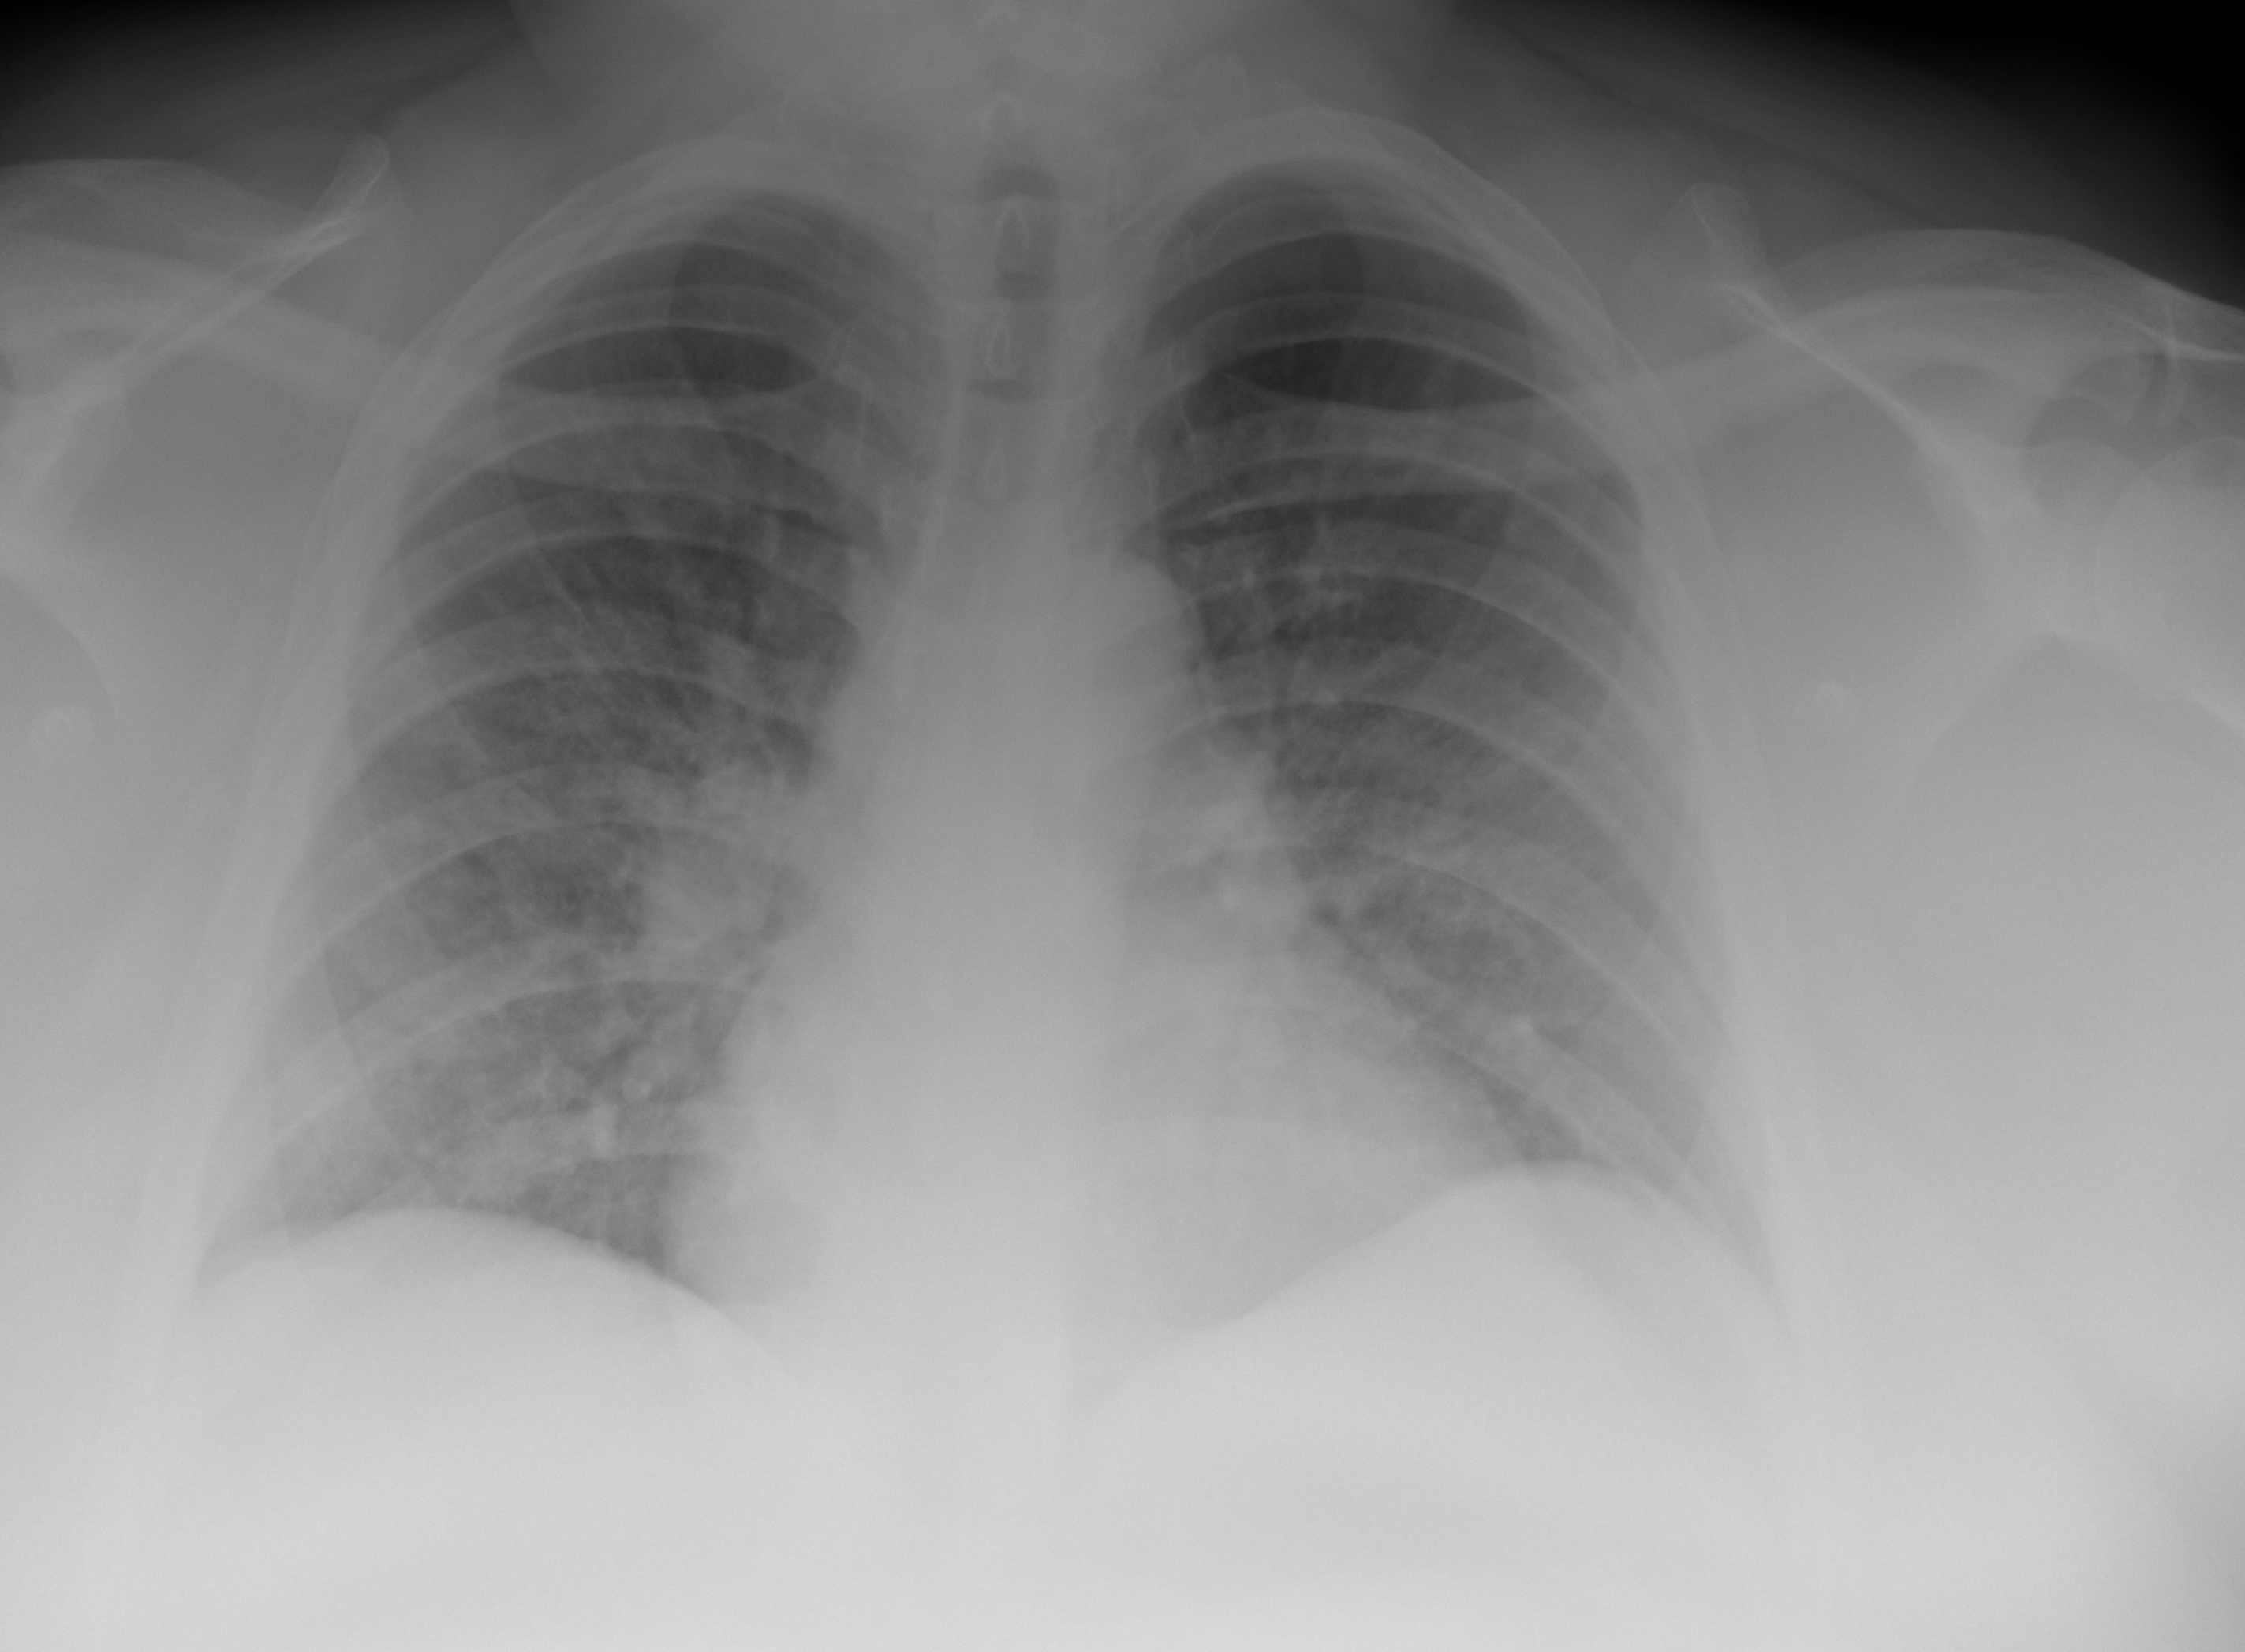
Portable chest radiograph, AP projection. Female patient, age 44 years; COVID-19 (test-positive).
Radiologist key findings (as recorded): Streaky opacities in bilateral mid and left lower lung. Patchy opacities in the right lower lung. No pleural effusion.